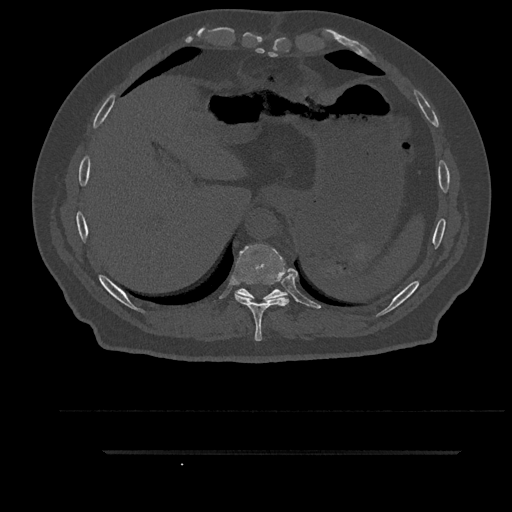
CT including the spine, one axial slice; slice 402 of 797 in the series (ordered by position); bone window (W 1800 / L 400 HU); 0.5 mm slice thickness; 512 × 512 image matrix, field of view 432 × 432 mm. Patient: male, 63 years. From the clinical record (not read from this slice): primary cancer: renal; vertebrae with lytic lesions (as recorded): T8.
Outlined on this slice (semi-automatically segmented with operator editing):
- T10 vertebra: bounding box (x1, y1, x2, y2) in pixels: (235, 288, 287, 300)
- T9 vertebra: (234, 244, 289, 341)